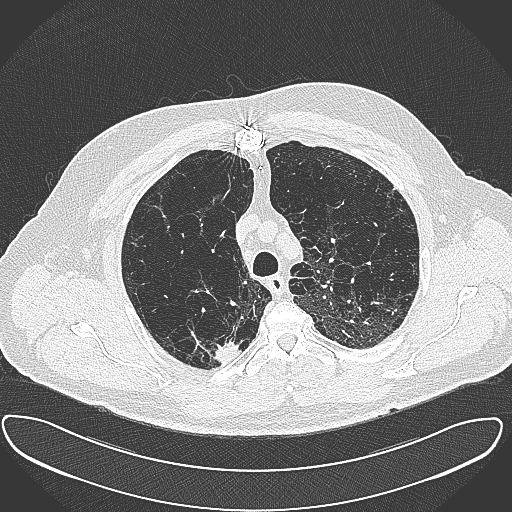
Chest CT (low-dose screening protocol), one axial image. Baseline annual screen. Lung window (W 1500 / L -600 HU). 1 mm slice thickness. Lung (sharp) reconstruction kernel (B80f). 120 kVp. Male participant, aged 60 years at enrolment. Current smoker at enrolment.
Expert reader's lesion annotation, bounding box <201,328,242,365> (left, top, right, bottom; pixels). The exam's reader record, not a measurement of the box and not confirmed to be the same lesion: non-calcified nodule or mass ≥4 mm, right upper lobe, 15 × 25 mm, spiculated (stellate) margins, soft tissue attenuation. Official screen result: positive, change unspecified: nodule(s) >= 4 mm or enlarging nodule(s), mass(es), or other non-specific abnormalities suspicious for lung cancer. Lung cancer was diagnosed 32 days after this screen: carcinoma, NOS, right upper lobe, moderately differentiated (G2), stage IB (AJCC 6th edition), 35 mm at pathology.